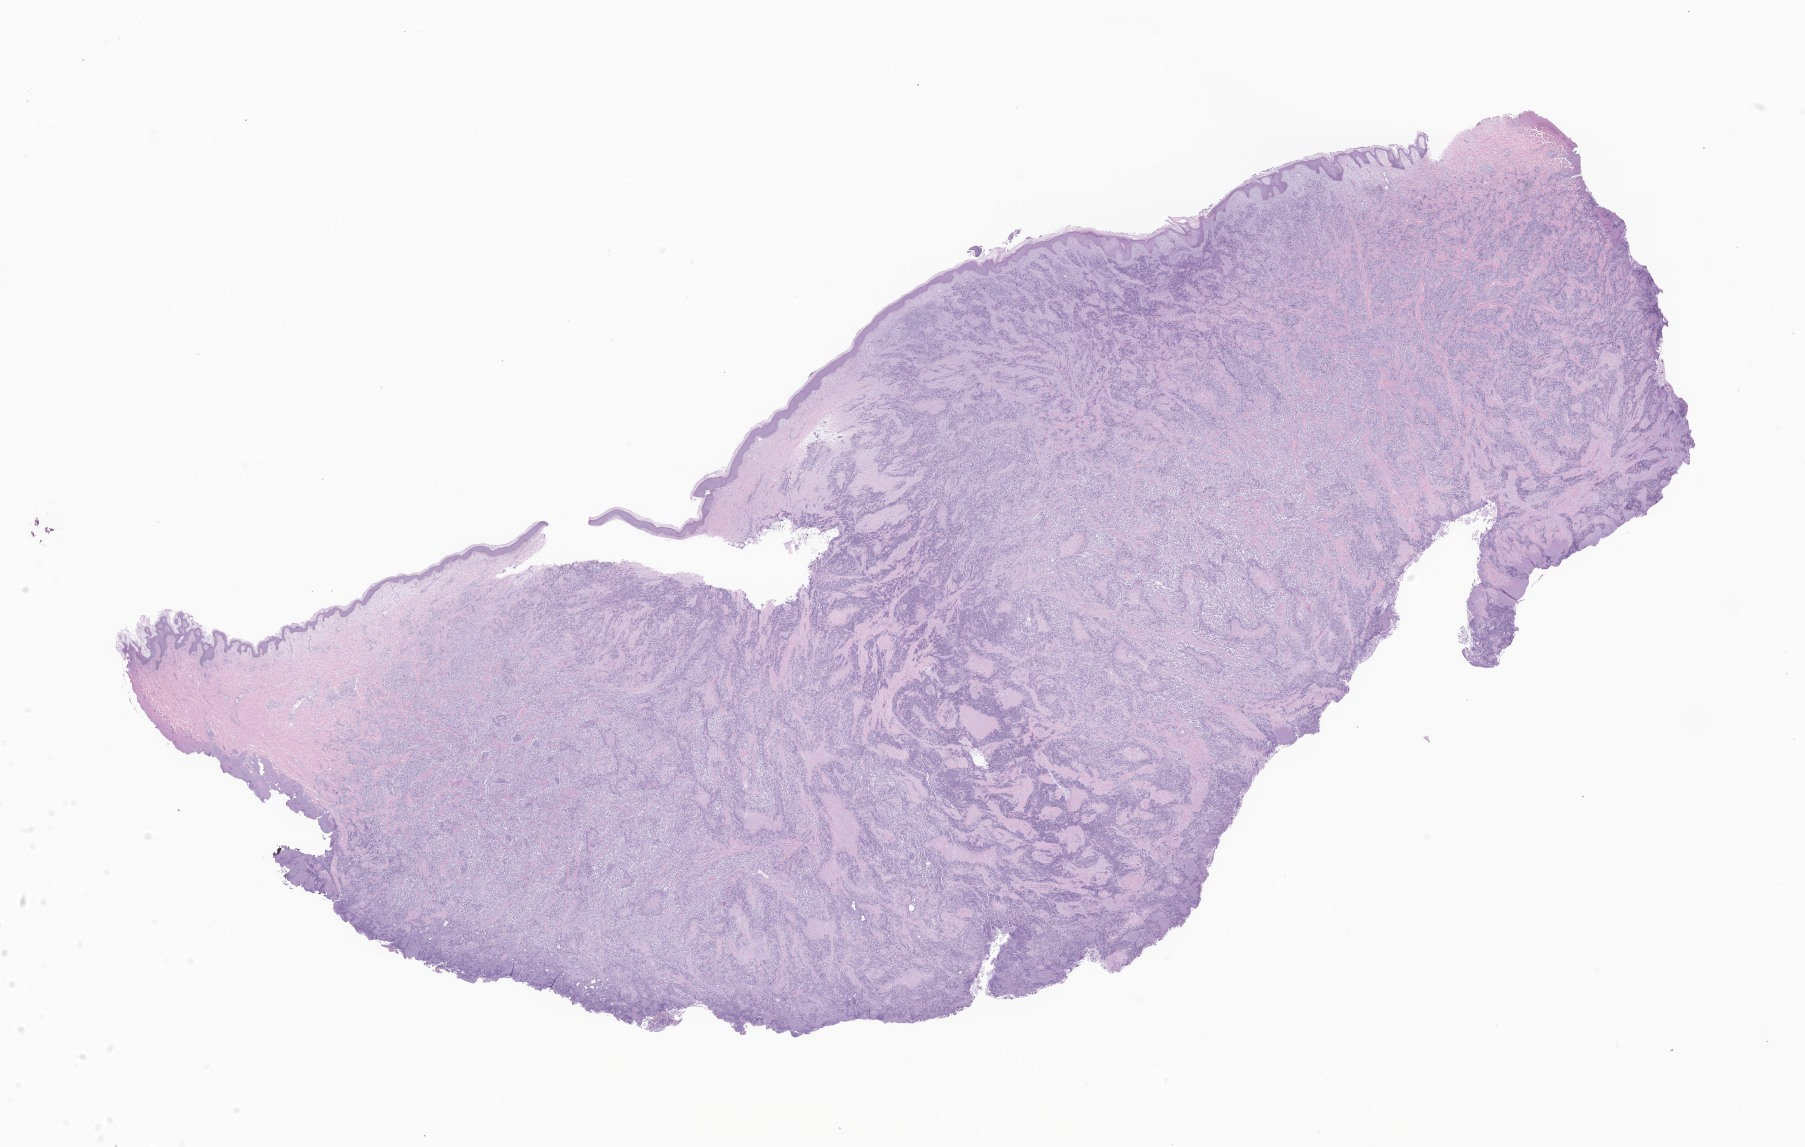
H&E whole-slide image of tumor tissue from the abdomen, whole scanned area (about 30.4 x 19.3 mm) shown as a low-resolution overview; formalin-fixed paraffin-embedded section. Male patient, age 182 months (15 years 2 months).
Diagnosis (ICD-O-3 morphology term): Desmoplastic small round cell tumor.